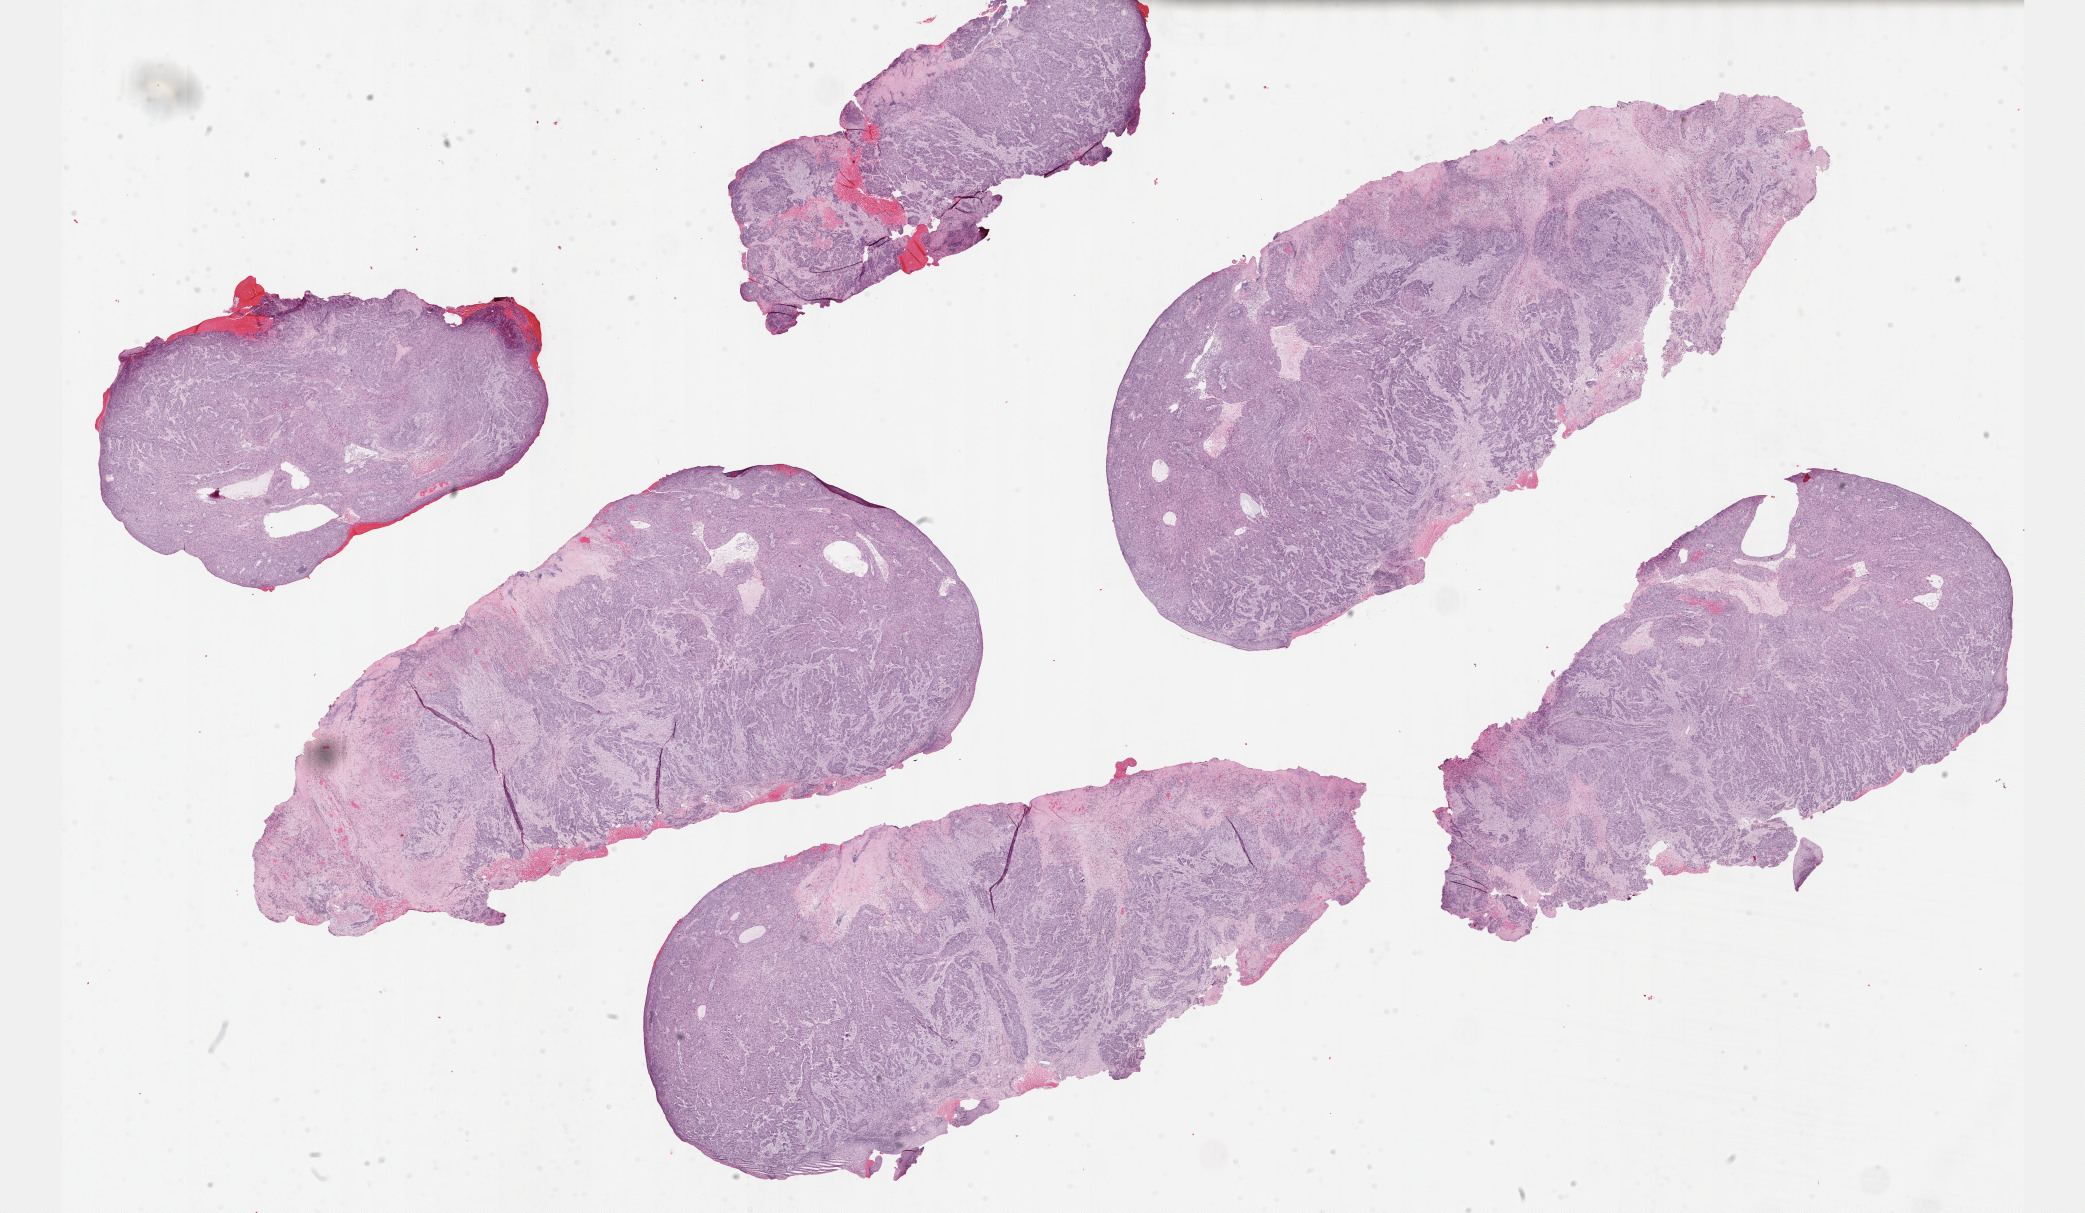
H&E-stained whole-slide image, low-resolution overview of the scanned area, about 33.7 x 19.6 mm (slide scanned at 40x); formalin-fixed paraffin-embedded (FFPE) diagnostic section; sample: primary tumour, cervix. Female patient; age at initial diagnosis 55 years. Histologic grade: GX (grade cannot be assessed).
Histologic diagnosis: Squamous cell carcinoma, large cell, nonkeratinizing, NOS (cervix uteri). FIGO stage: I.